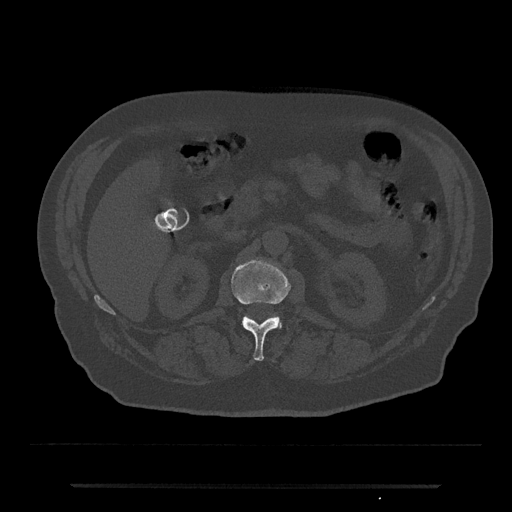
CT including the spine, one axial slice; slice 522 of 797 in the series (ordered by position); 120 kVp; bone window (W 1800 / L 400 HU); 512 × 512 image matrix. Male patient, age 80 years. Case-level facts recorded for this patient, not image findings: primary cancer: prostate; vertebrae with lytic lesions (as recorded): L1, T11.
Structures marked on this image (semi-automatically segmented with operator editing):
- L1 vertebra: box from (x=231, y=260) to (x=291, y=361) px
- L2 vertebra: (x=279, y=318)–(x=282, y=328)